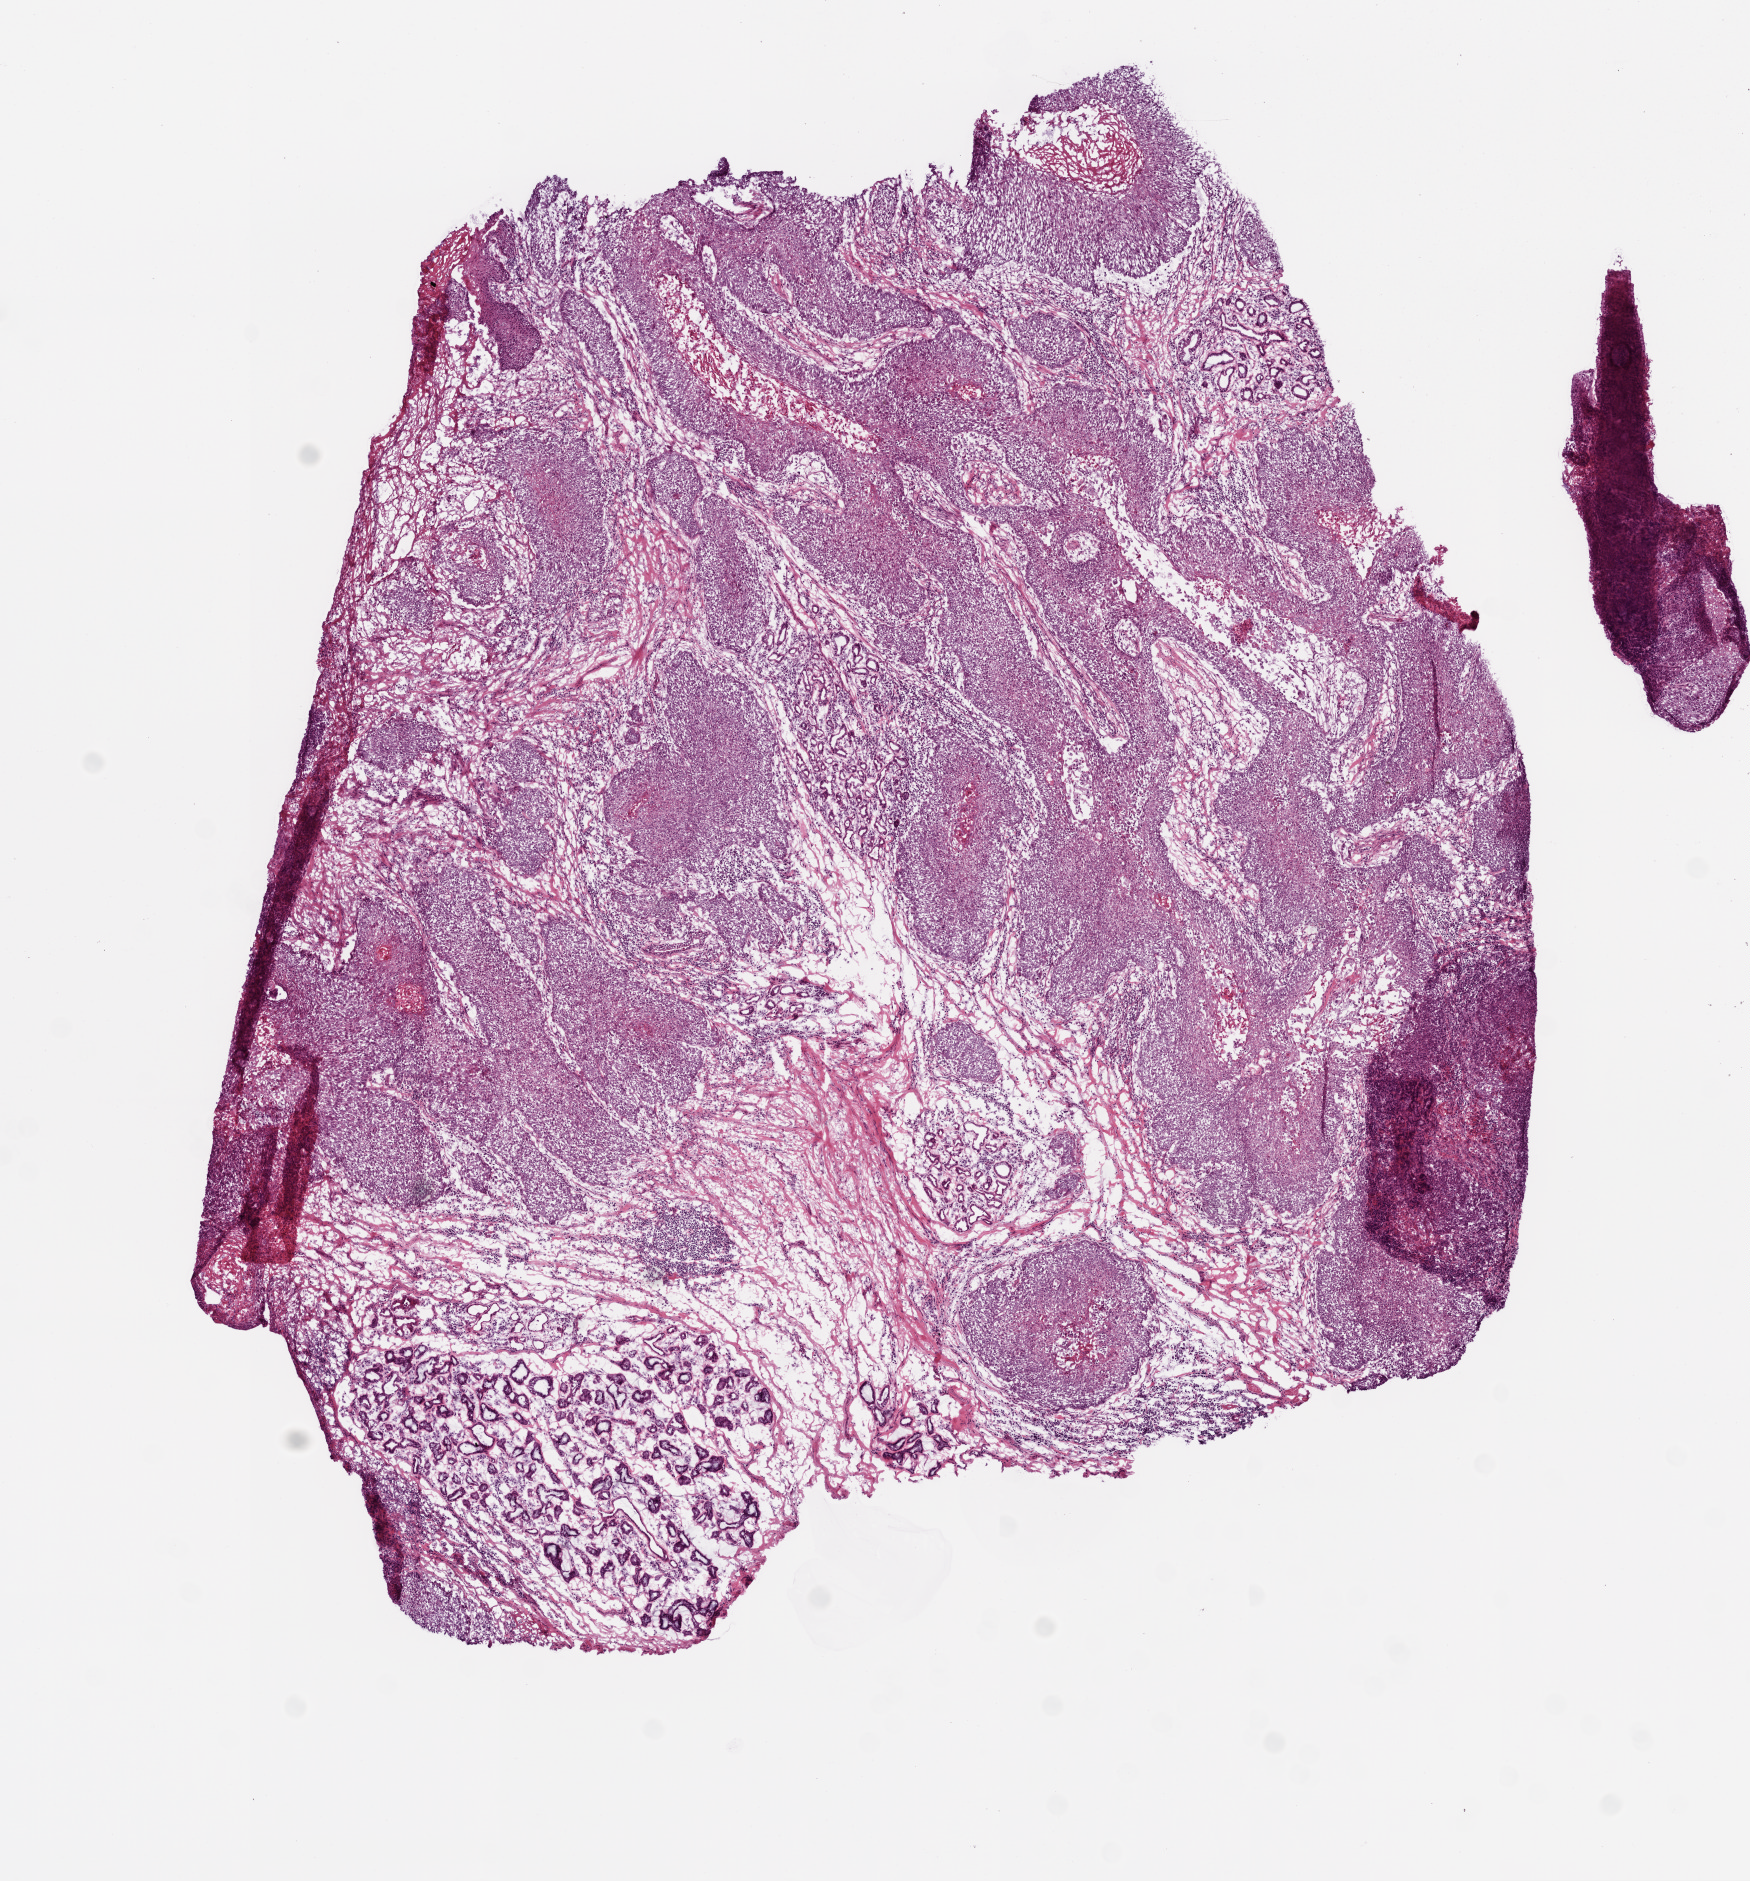
Digitized Hematoxylin and eosin (H&E) stained tissue section (whole slide) — shown as a low-resolution overview of the whole scanned area (about 7.0 x 7.5 mm), frozen section from the bottom of the tissue portion, primary tumour sample from the head and neck. Patient: male, age at initial diagnosis 68 years. Histologic grade: G2 (moderately differentiated). Composition of this section per pathologist review: tumour cells 70%, tumour nuclei 80%, normal cells 10%, stromal cells 15%, necrosis 0%.
* AJCC pathologic stage: IVA (6th edition)
* pathologic diagnosis: Squamous cell carcinoma, NOS (larynx, NOS)